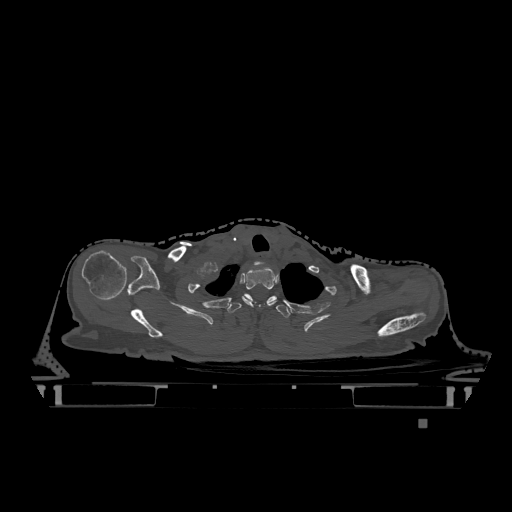
CT including the spine, one axial slice. Position 986 of 1317 along the scan axis. Bone window (W 1800 / L 400 HU). 0.5 mm slice thickness. 512 × 512 image matrix, field of view 500 × 500 mm. Patient: female, 74 years. From the clinical record (not read from this slice): primary cancer: lung.
Structures marked on this image (semi-automatically segmented with operator editing):
- T1 vertebra: box from (x=241, y=267) to (x=277, y=307) px
- T2 vertebra: (x=228, y=294)–(x=291, y=318)